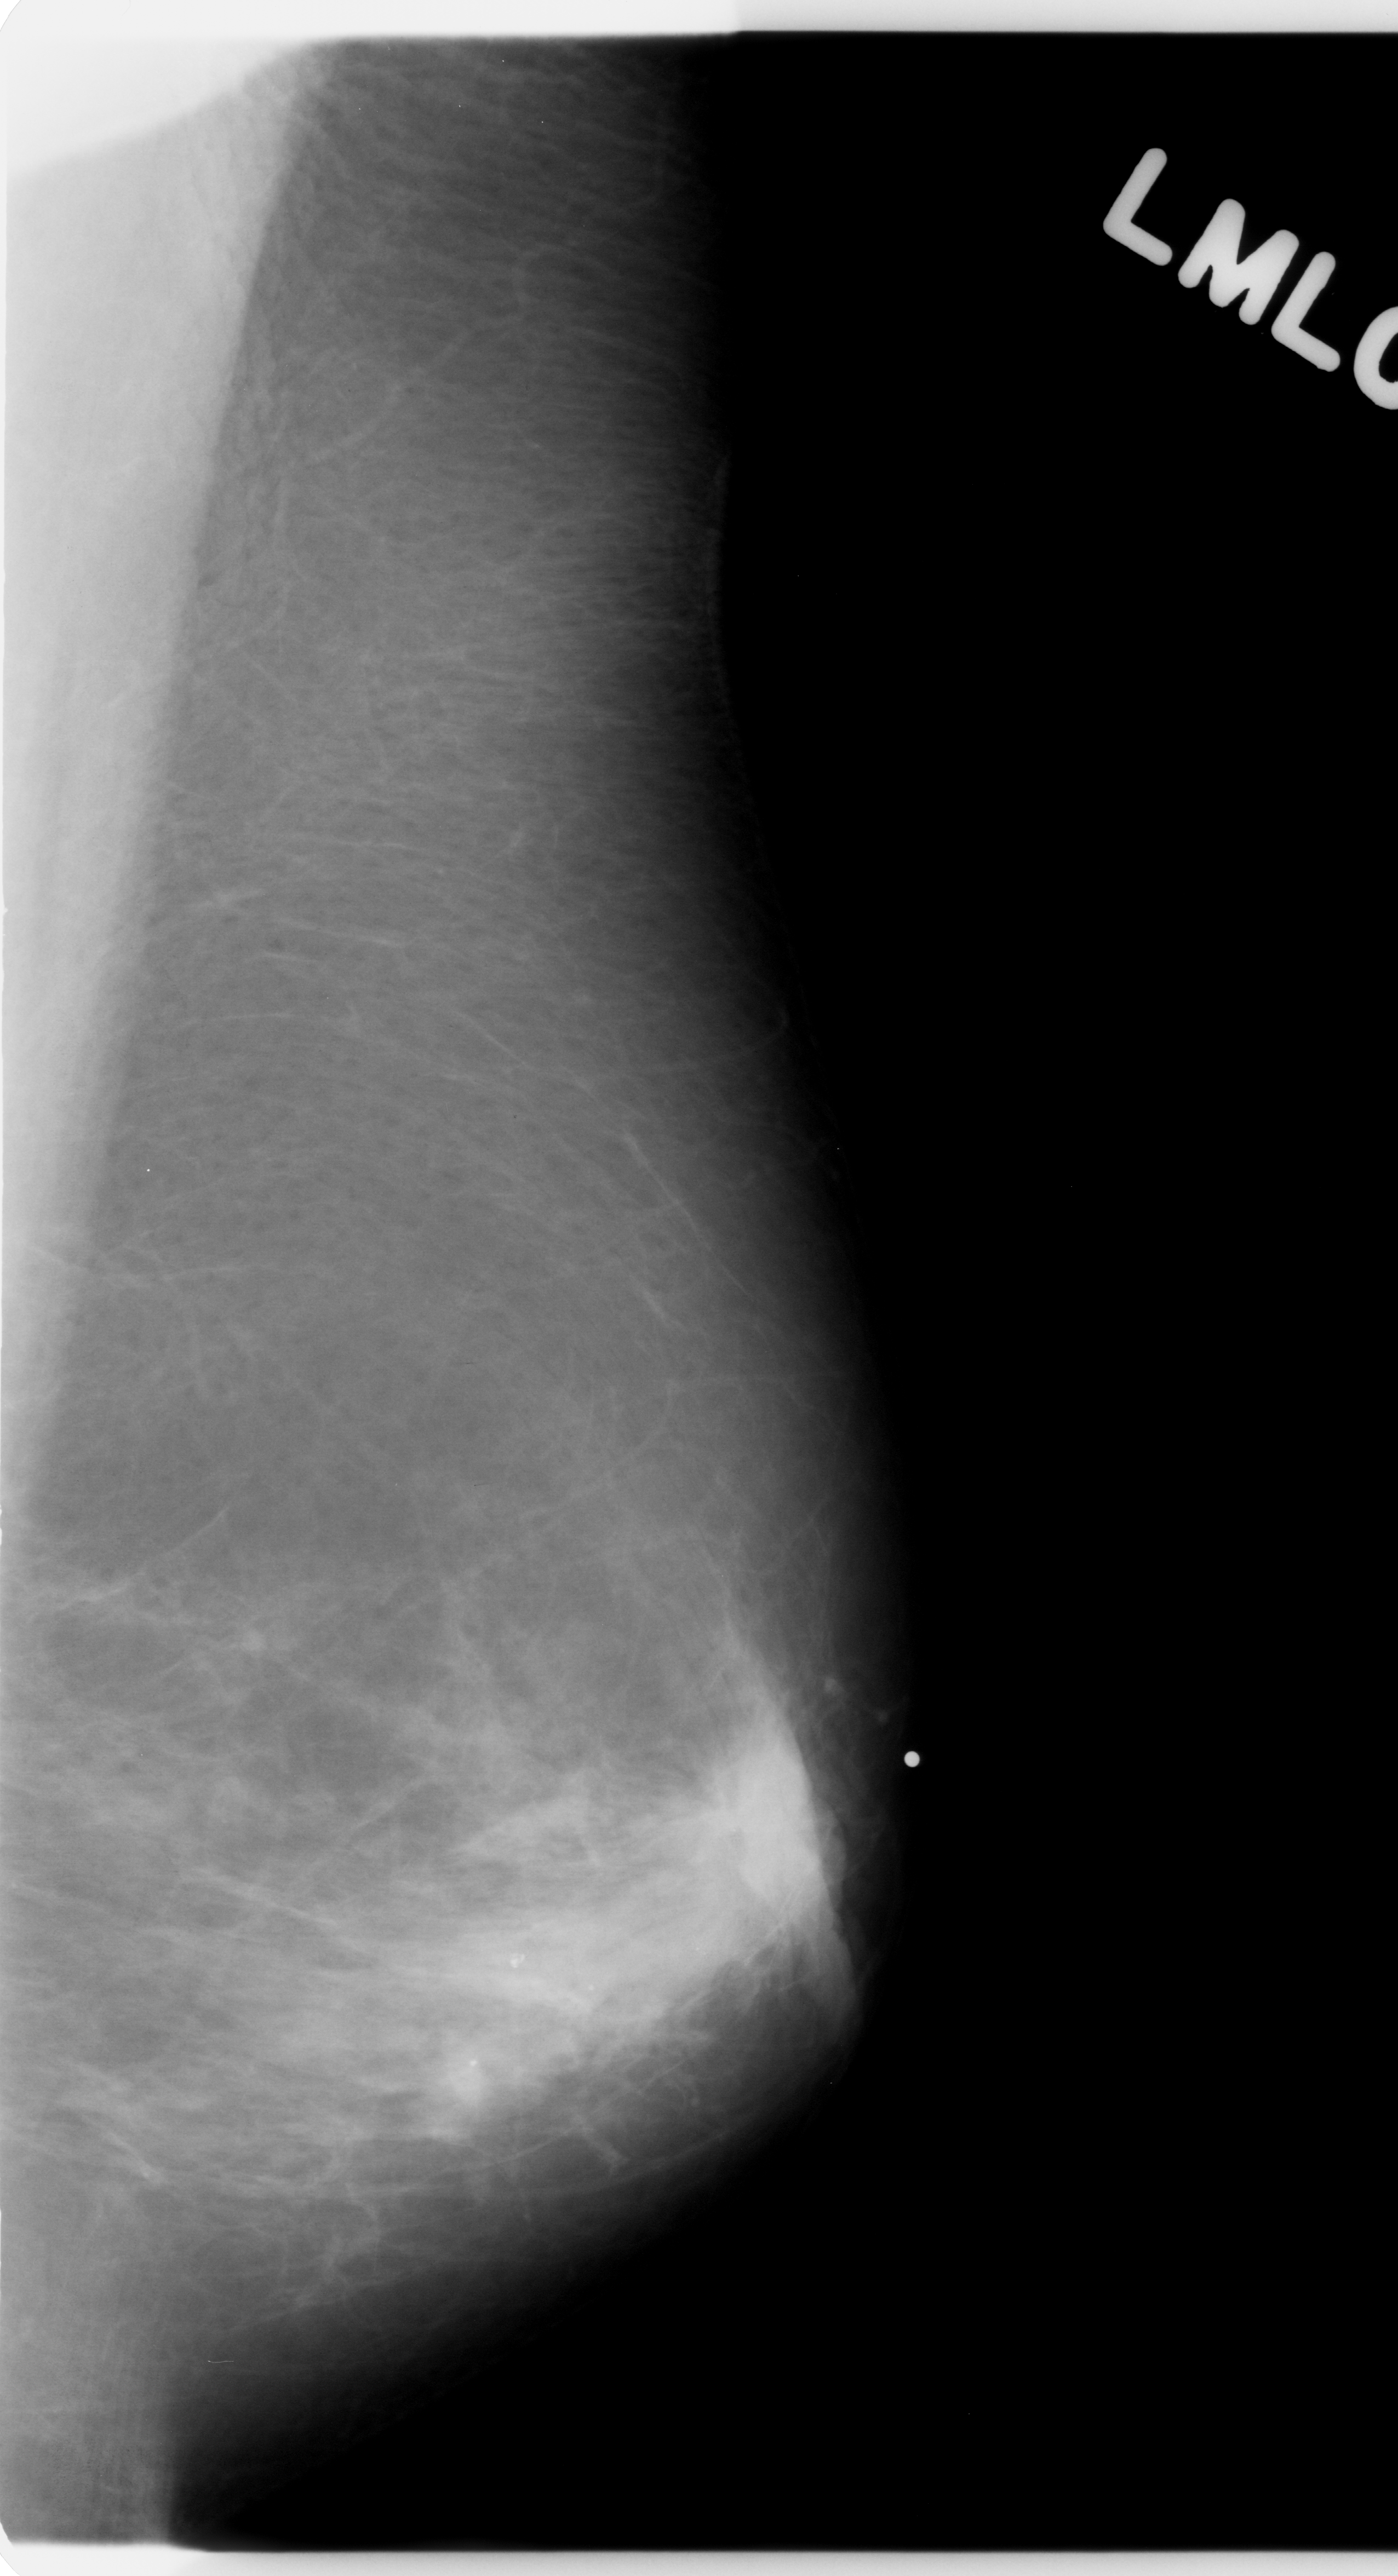
Mammogram (digitized film); left breast; mediolateral oblique (MLO) view; breast composition: scattered fibroglandular densities (BI-RADS density category 2 of 4); 1398 × 2576 image matrix.
Marked abnormalities (boxes around the expert regions of interest):
- mass, shape irregular, margins spiculated; BI-RADS assessment category 5; pathology result (as recorded, not read from the image): malignant: bounding box <614,1625,895,2049> (left, top, right, bottom; pixels)